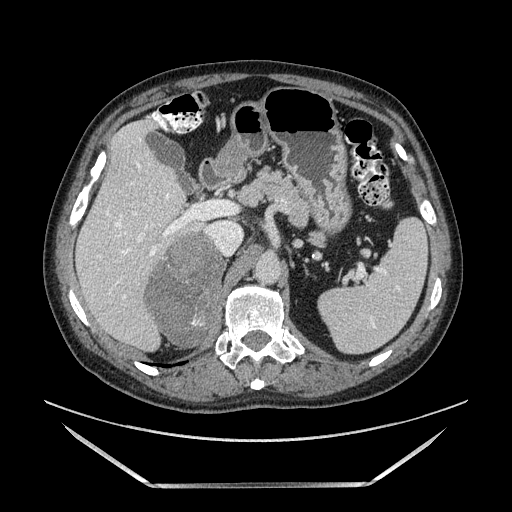
Contrast-enhanced abdominal CT, one axial slice; slice 92 of 185 in the series (ordered by position); soft-tissue window (W 400 / L 40 HU); 512 × 512 image matrix. Male patient. Case-level facts recorded for this patient, not image findings: diagnosis: adrenocortical carcinoma; tumour side: right adrenal; tumour size at pathology: 10.3 cm; Ki-67 index: 20 %; stage (as recorded): 3.
Outlined on this slice (semi-automatic segmentation, software-assisted and operator-edited):
- mass: bounding box (x1, y1, x2, y2) in pixels: (148, 231, 226, 339)